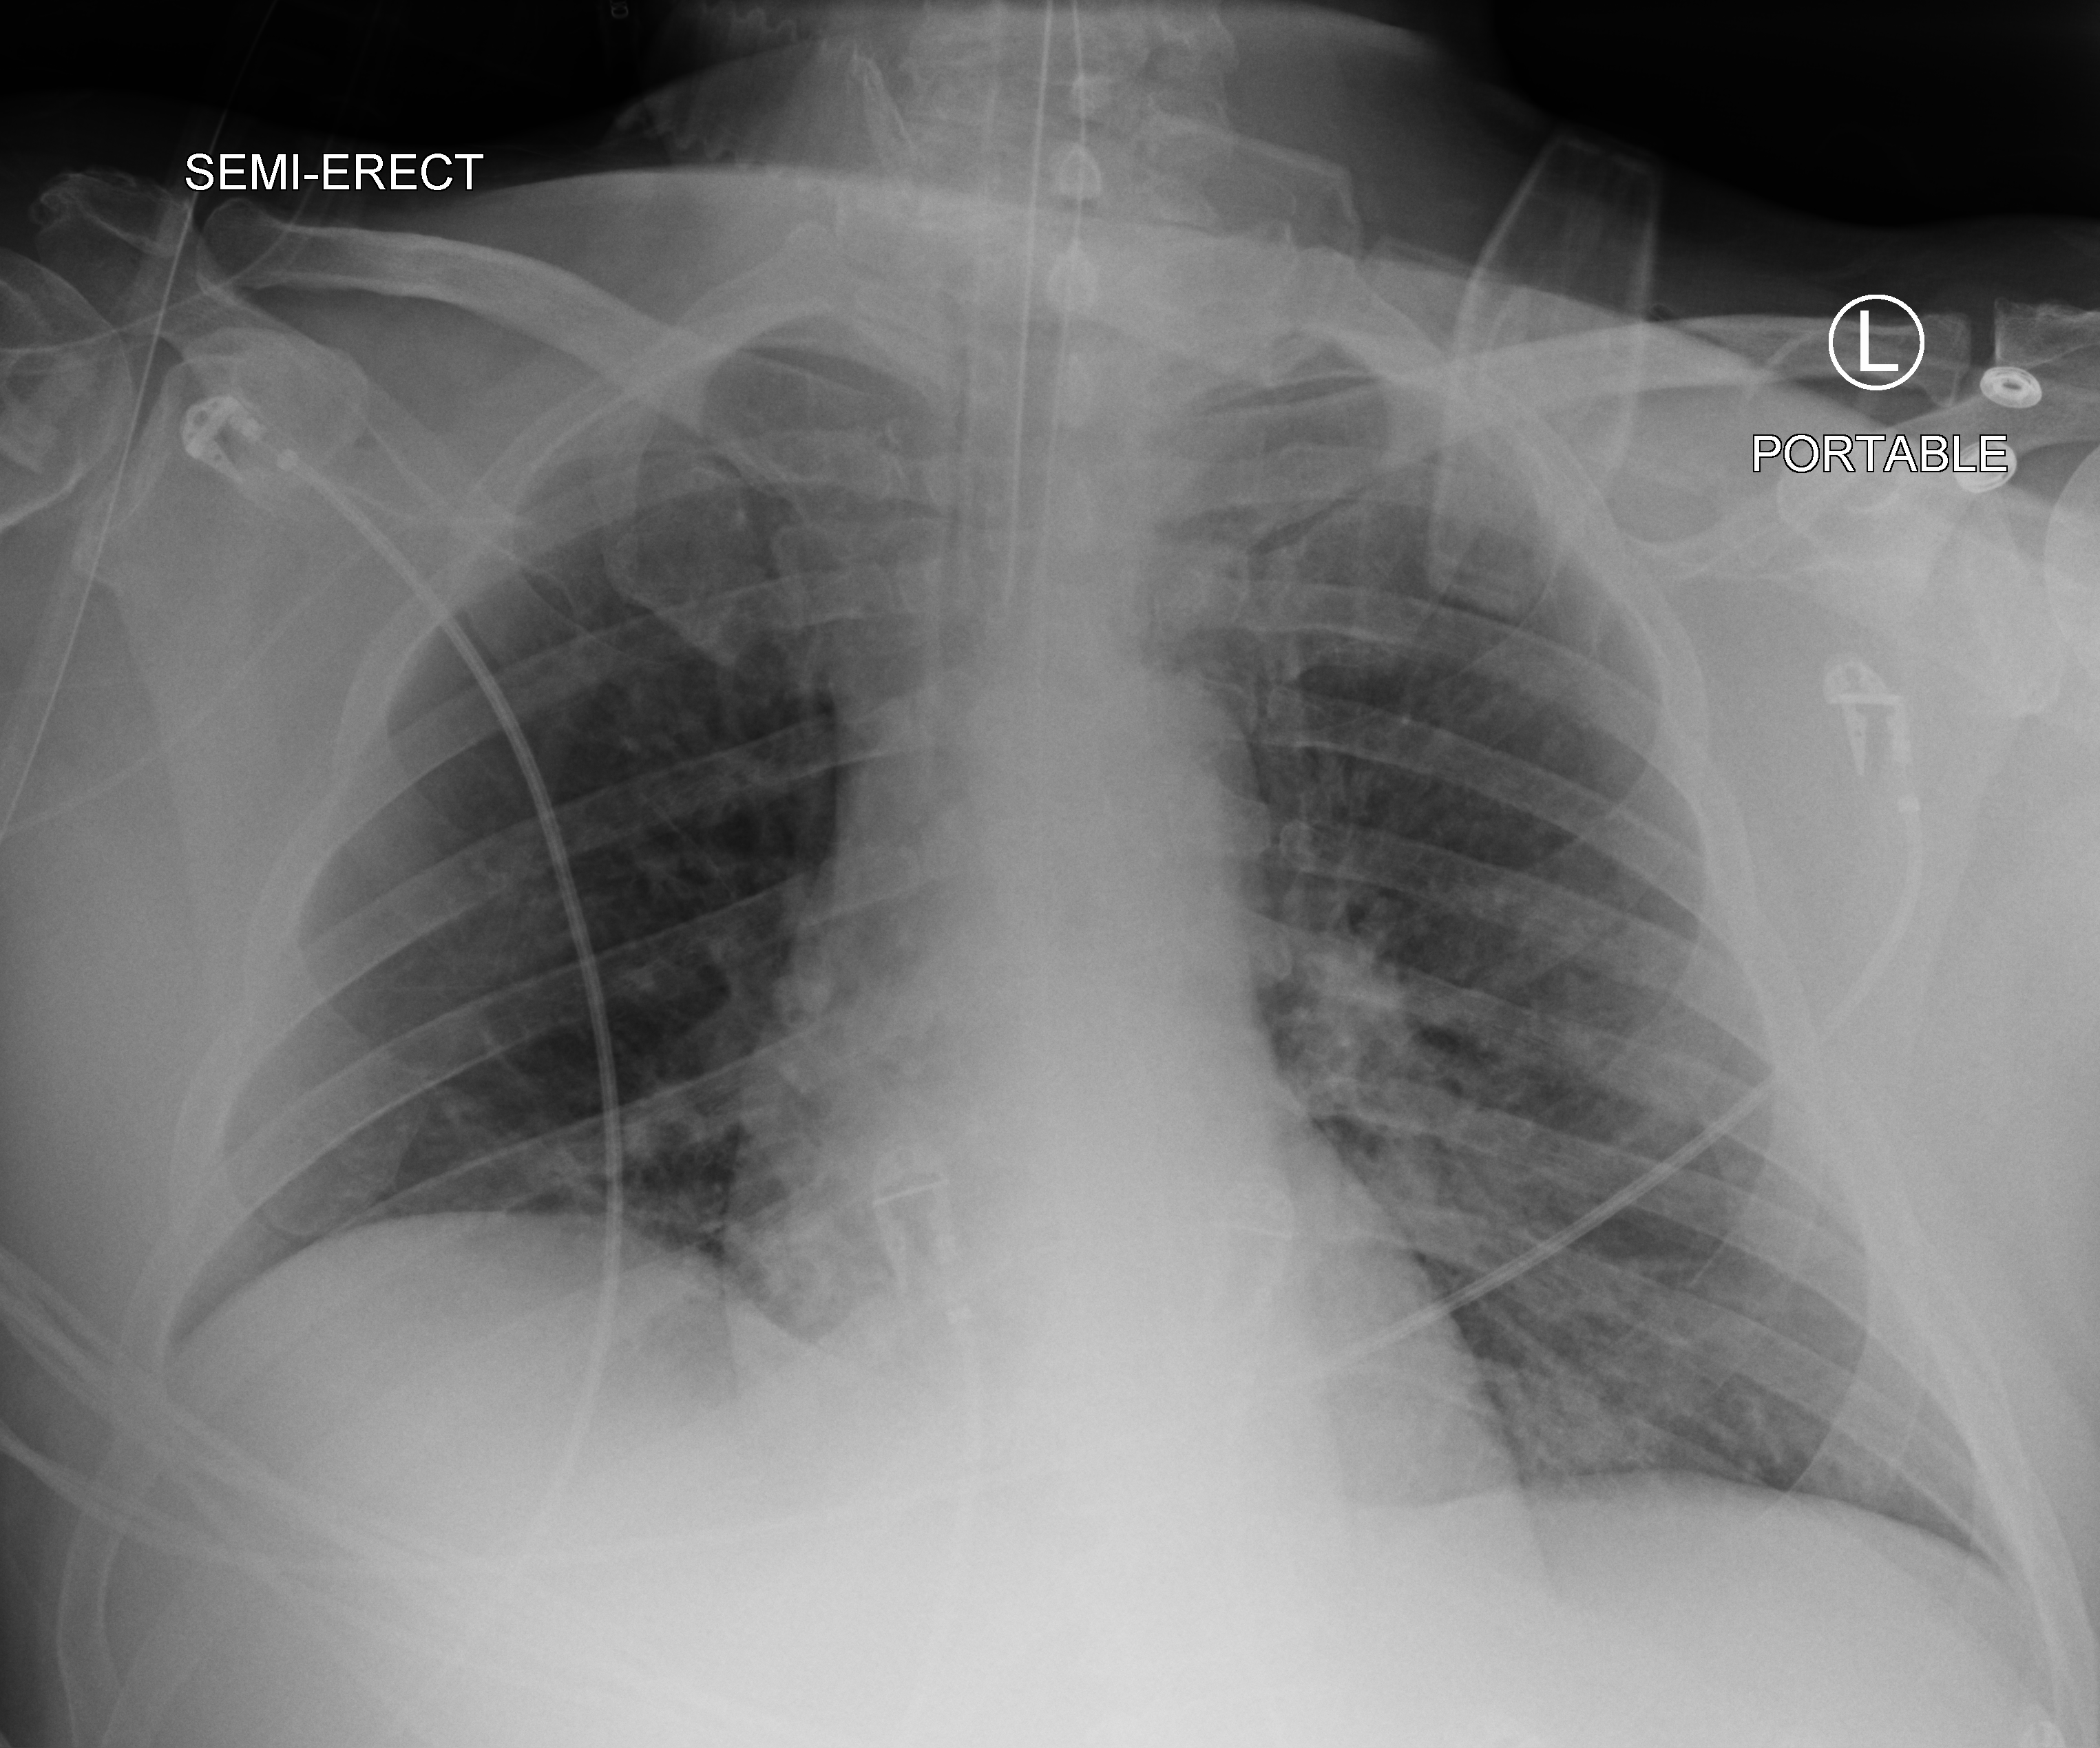
Portable chest radiograph; anteroposterior (AP) projection. Male patient hospitalised with COVID-19, age 18–59 years.
Admission-level facts for this patient (not findings on this image; timing relative to this image not recorded): smoking status (admission record): never; mechanically ventilated during this hospital stay: yes.